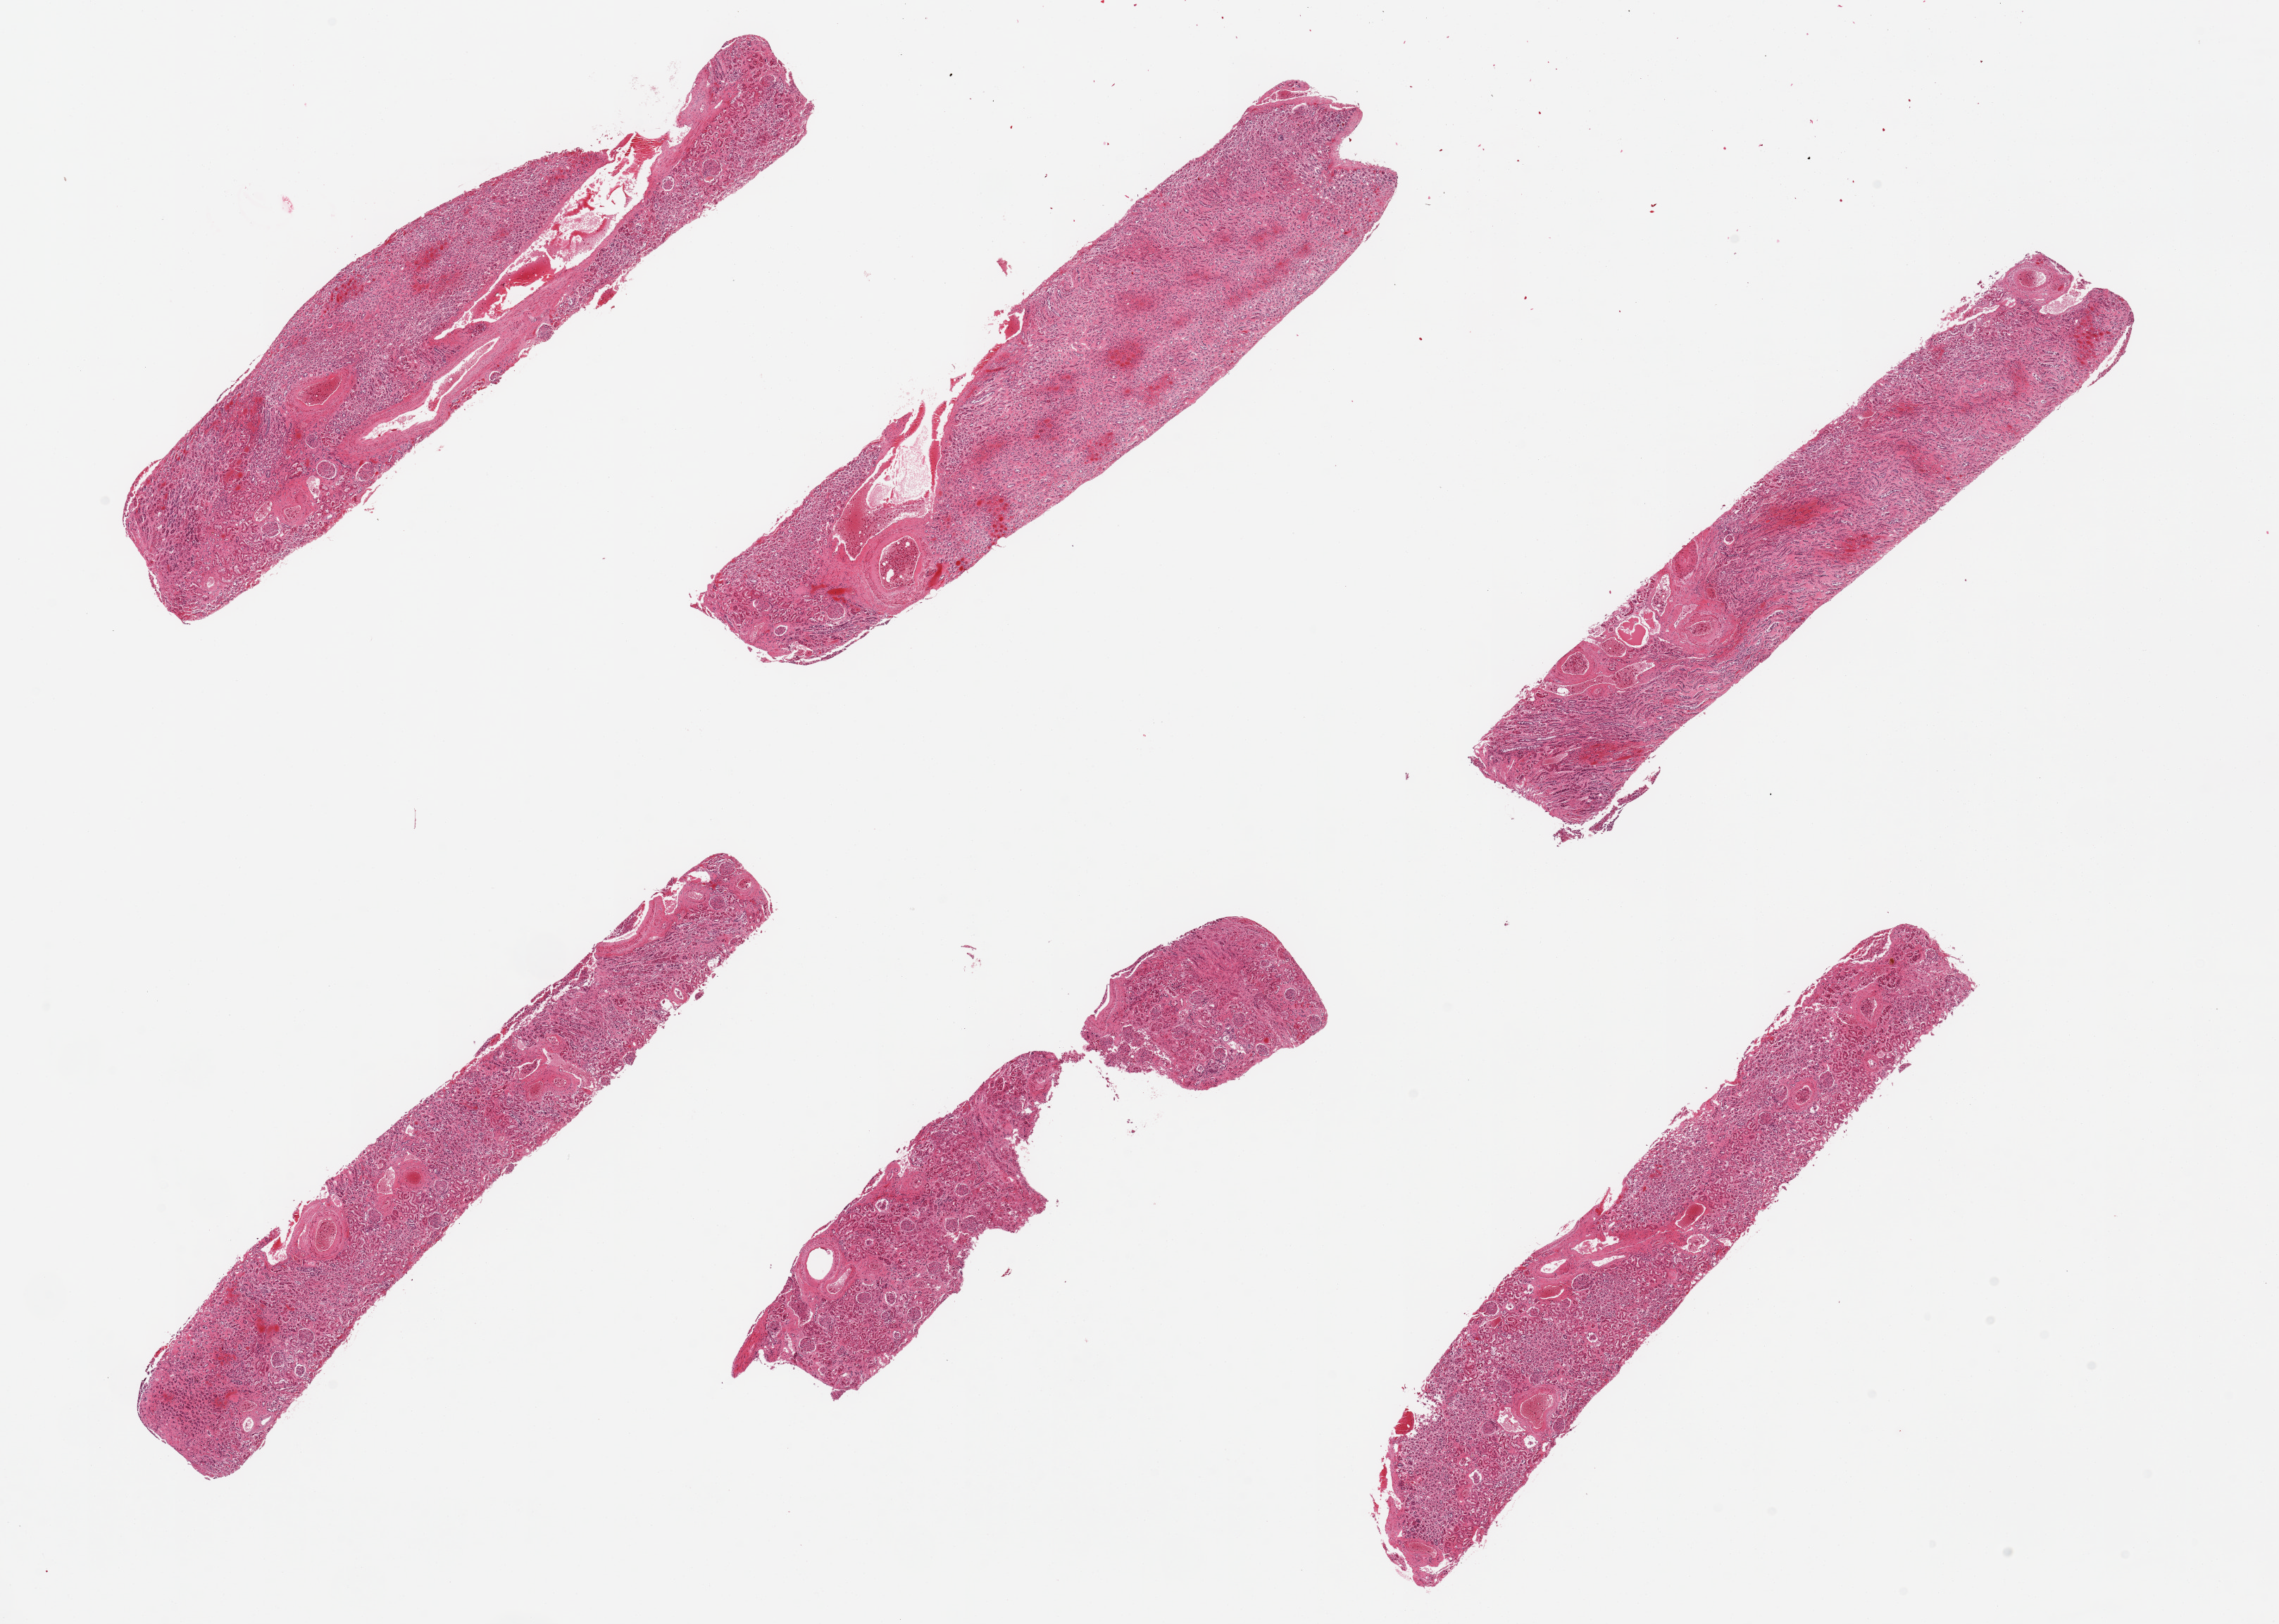
Whole-slide image, H&E stain, brightfield, a low-resolution overview of the entire scanned area, about 25.6 x 18.2 mm (from a 20x scan); PAXgene-fixed, paraffin-embedded tissue; sampled site (target tissue): renal cortex; donor tissue sample. Donor sex: male.
Reviewer comment on this tissue sample: 6 pieces; 3 pieces have >50% medulla.